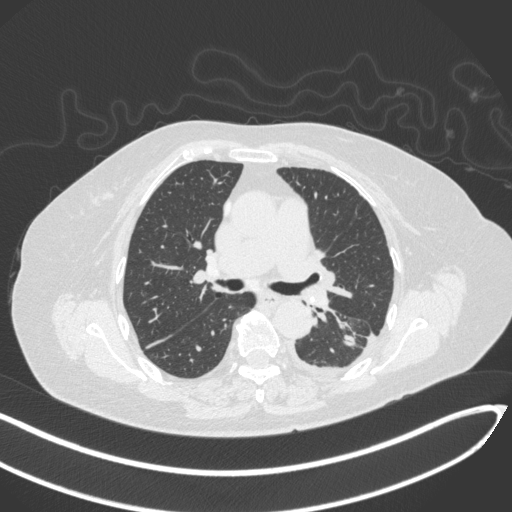
Chest CT, one axial slice; position 190 of 270 along the scan axis; lung window (W 1500 / L -600 HU); 1 mm slice thickness; 512 × 512 image matrix, field of view 400 × 400 mm. Patient: female, 76 years. Case-level facts recorded for this patient, not image findings: clinical TNM (as recorded): T1c N0 M0.
Outlined on this slice (rectangle marked by the reading radiologist):
- lung tumour (recorded histology: adenocarcinoma): box from (x=343, y=332) to (x=359, y=347) px